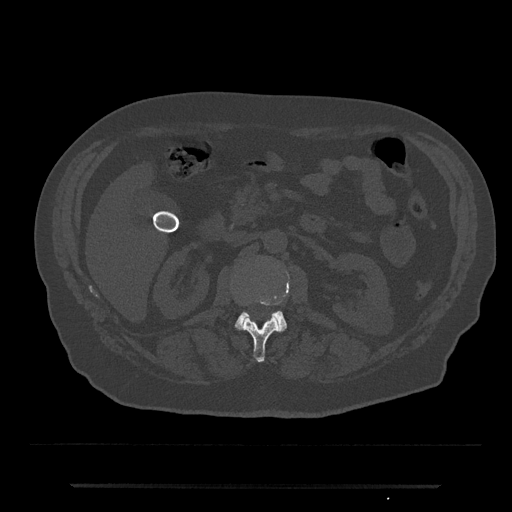
CT including the spine, one axial slice; reconstruction kernel Br40s/3; bone window (W 1800 / L 400 HU); 512 × 512 image matrix. Patient: male, 80 years. Case-level facts recorded for this patient, not image findings: primary cancer: prostate; vertebrae with lytic lesions (as recorded): L1, T11.
Structures marked on this image (semi-automatically segmented with operator editing):
- L1 vertebra: bounding box <243,301,280,362> (left, top, right, bottom; pixels)
- L2 vertebra: <235,296,288,332>